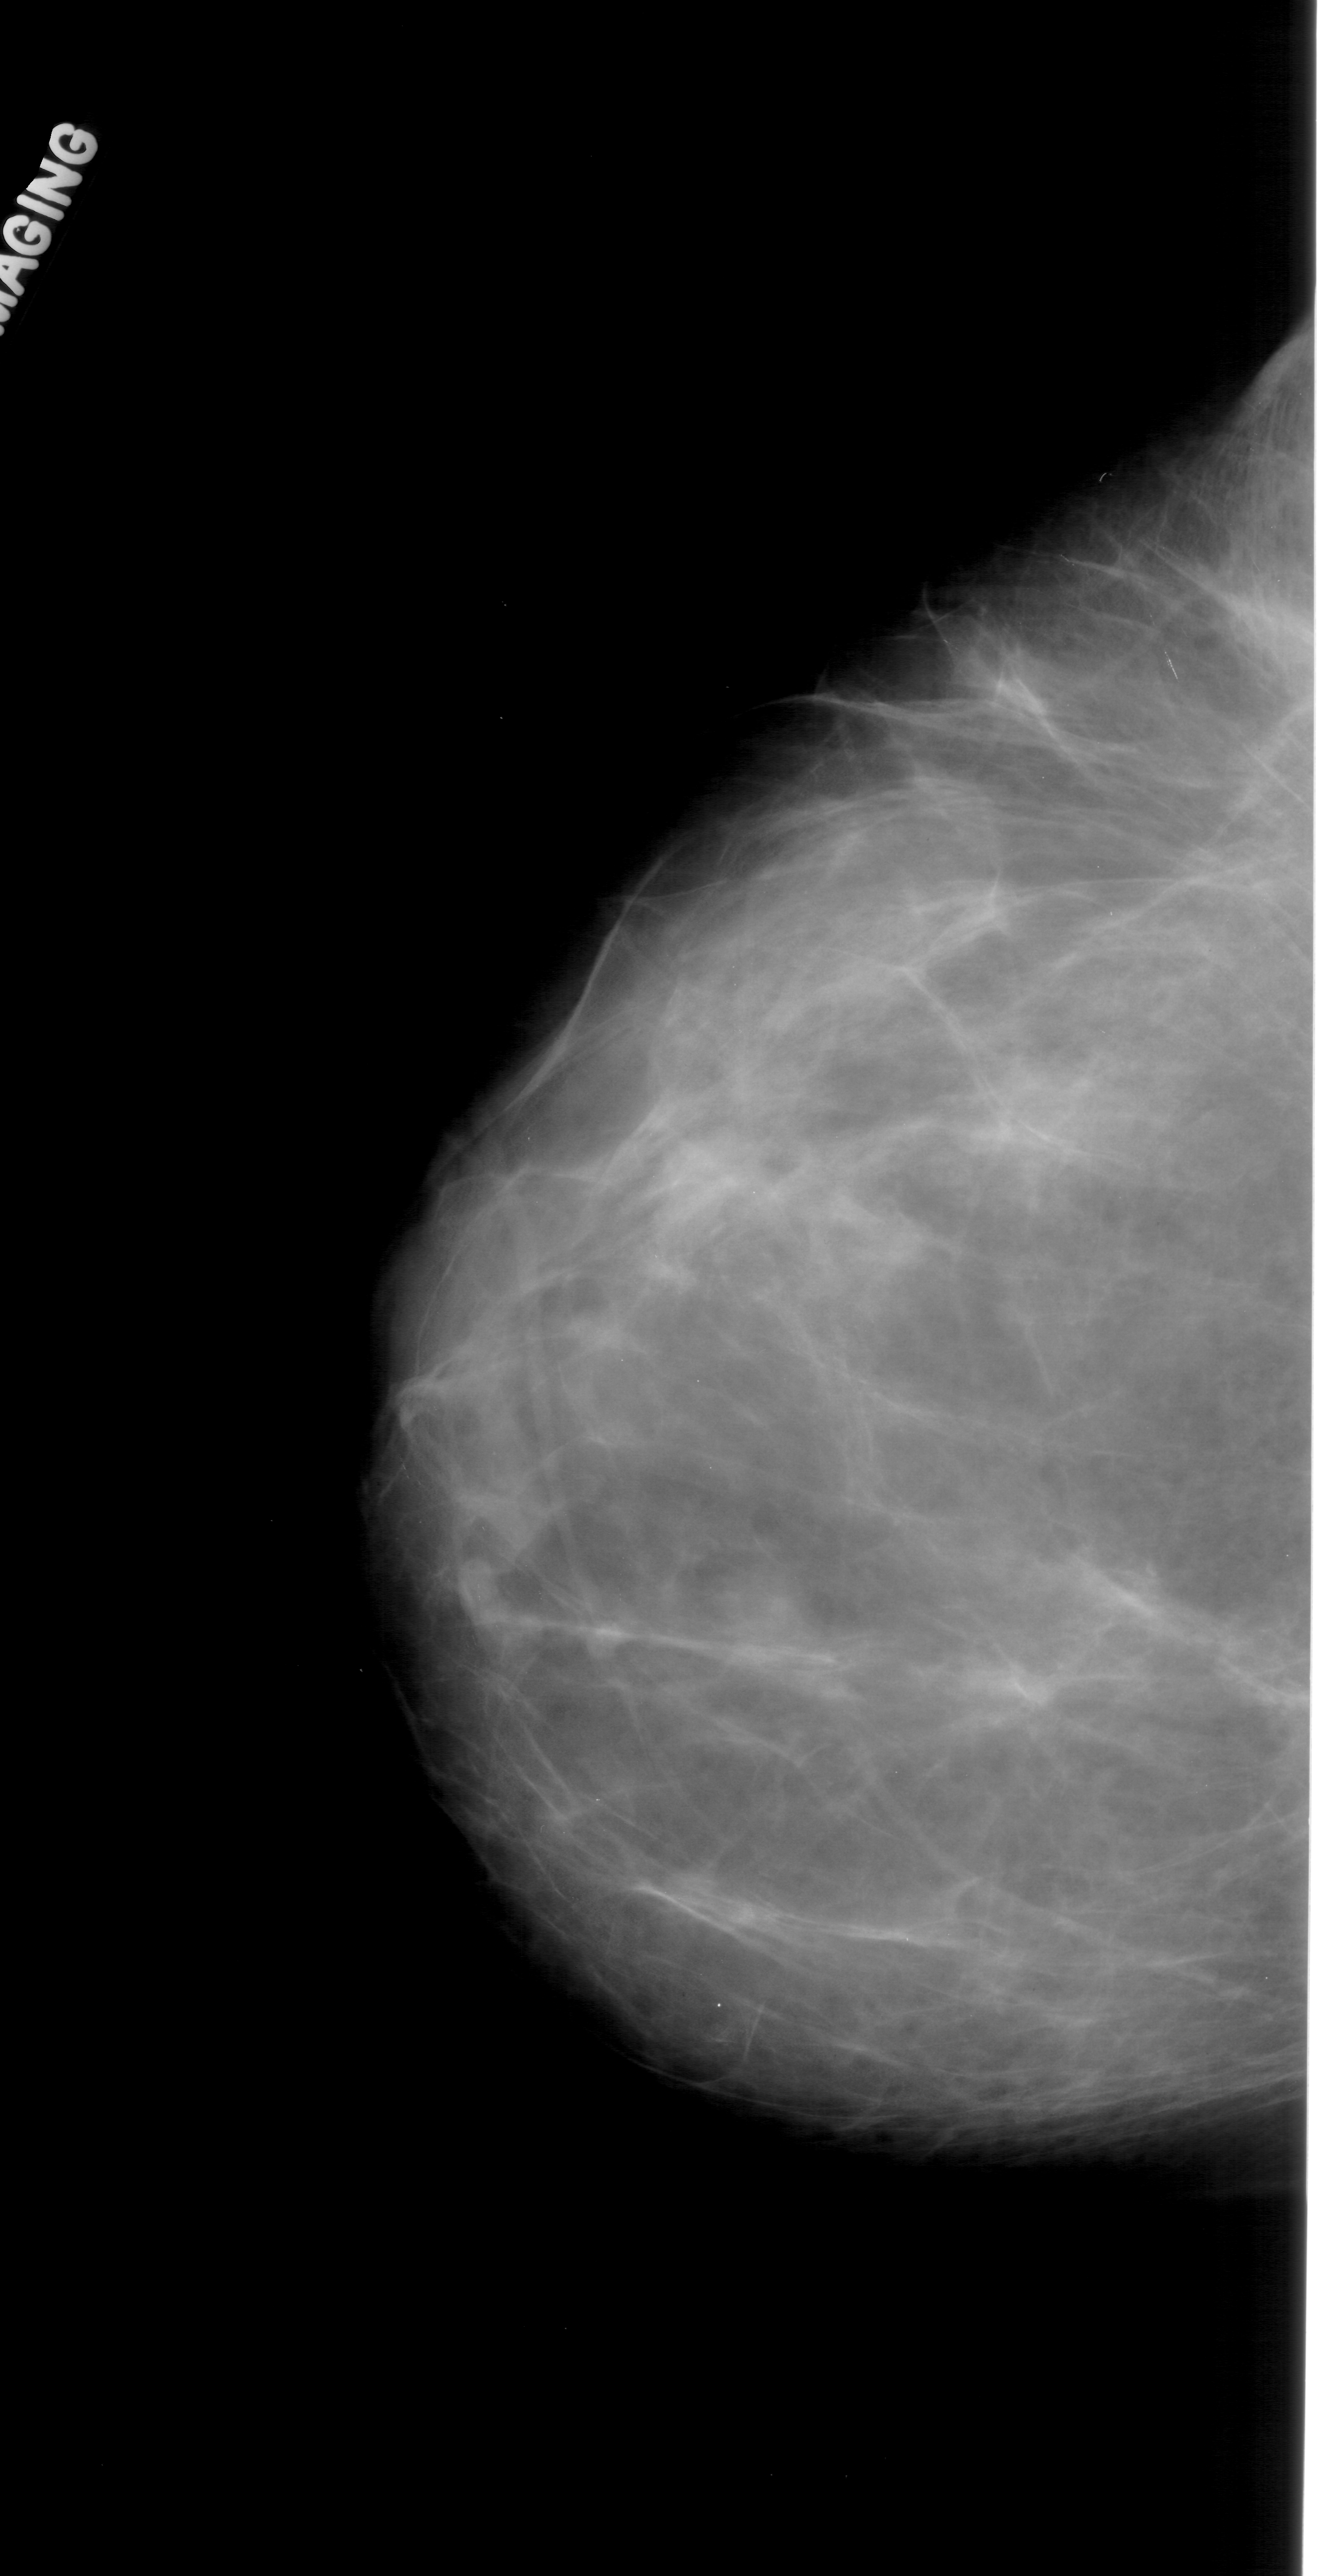
Mammogram (digitized film); left breast; CC view; breast composition: almost entirely fatty (BI-RADS density category 1 of 4); 1327 × 2576 image matrix.
Expert-marked regions of interest on this film, with their recorded descriptors:
- mass, shape lobulated, margins circumscribed; BI-RADS assessment category 4; pathology (as recorded): benign: bounding box <455,1573,552,1661> (left, top, right, bottom; pixels)